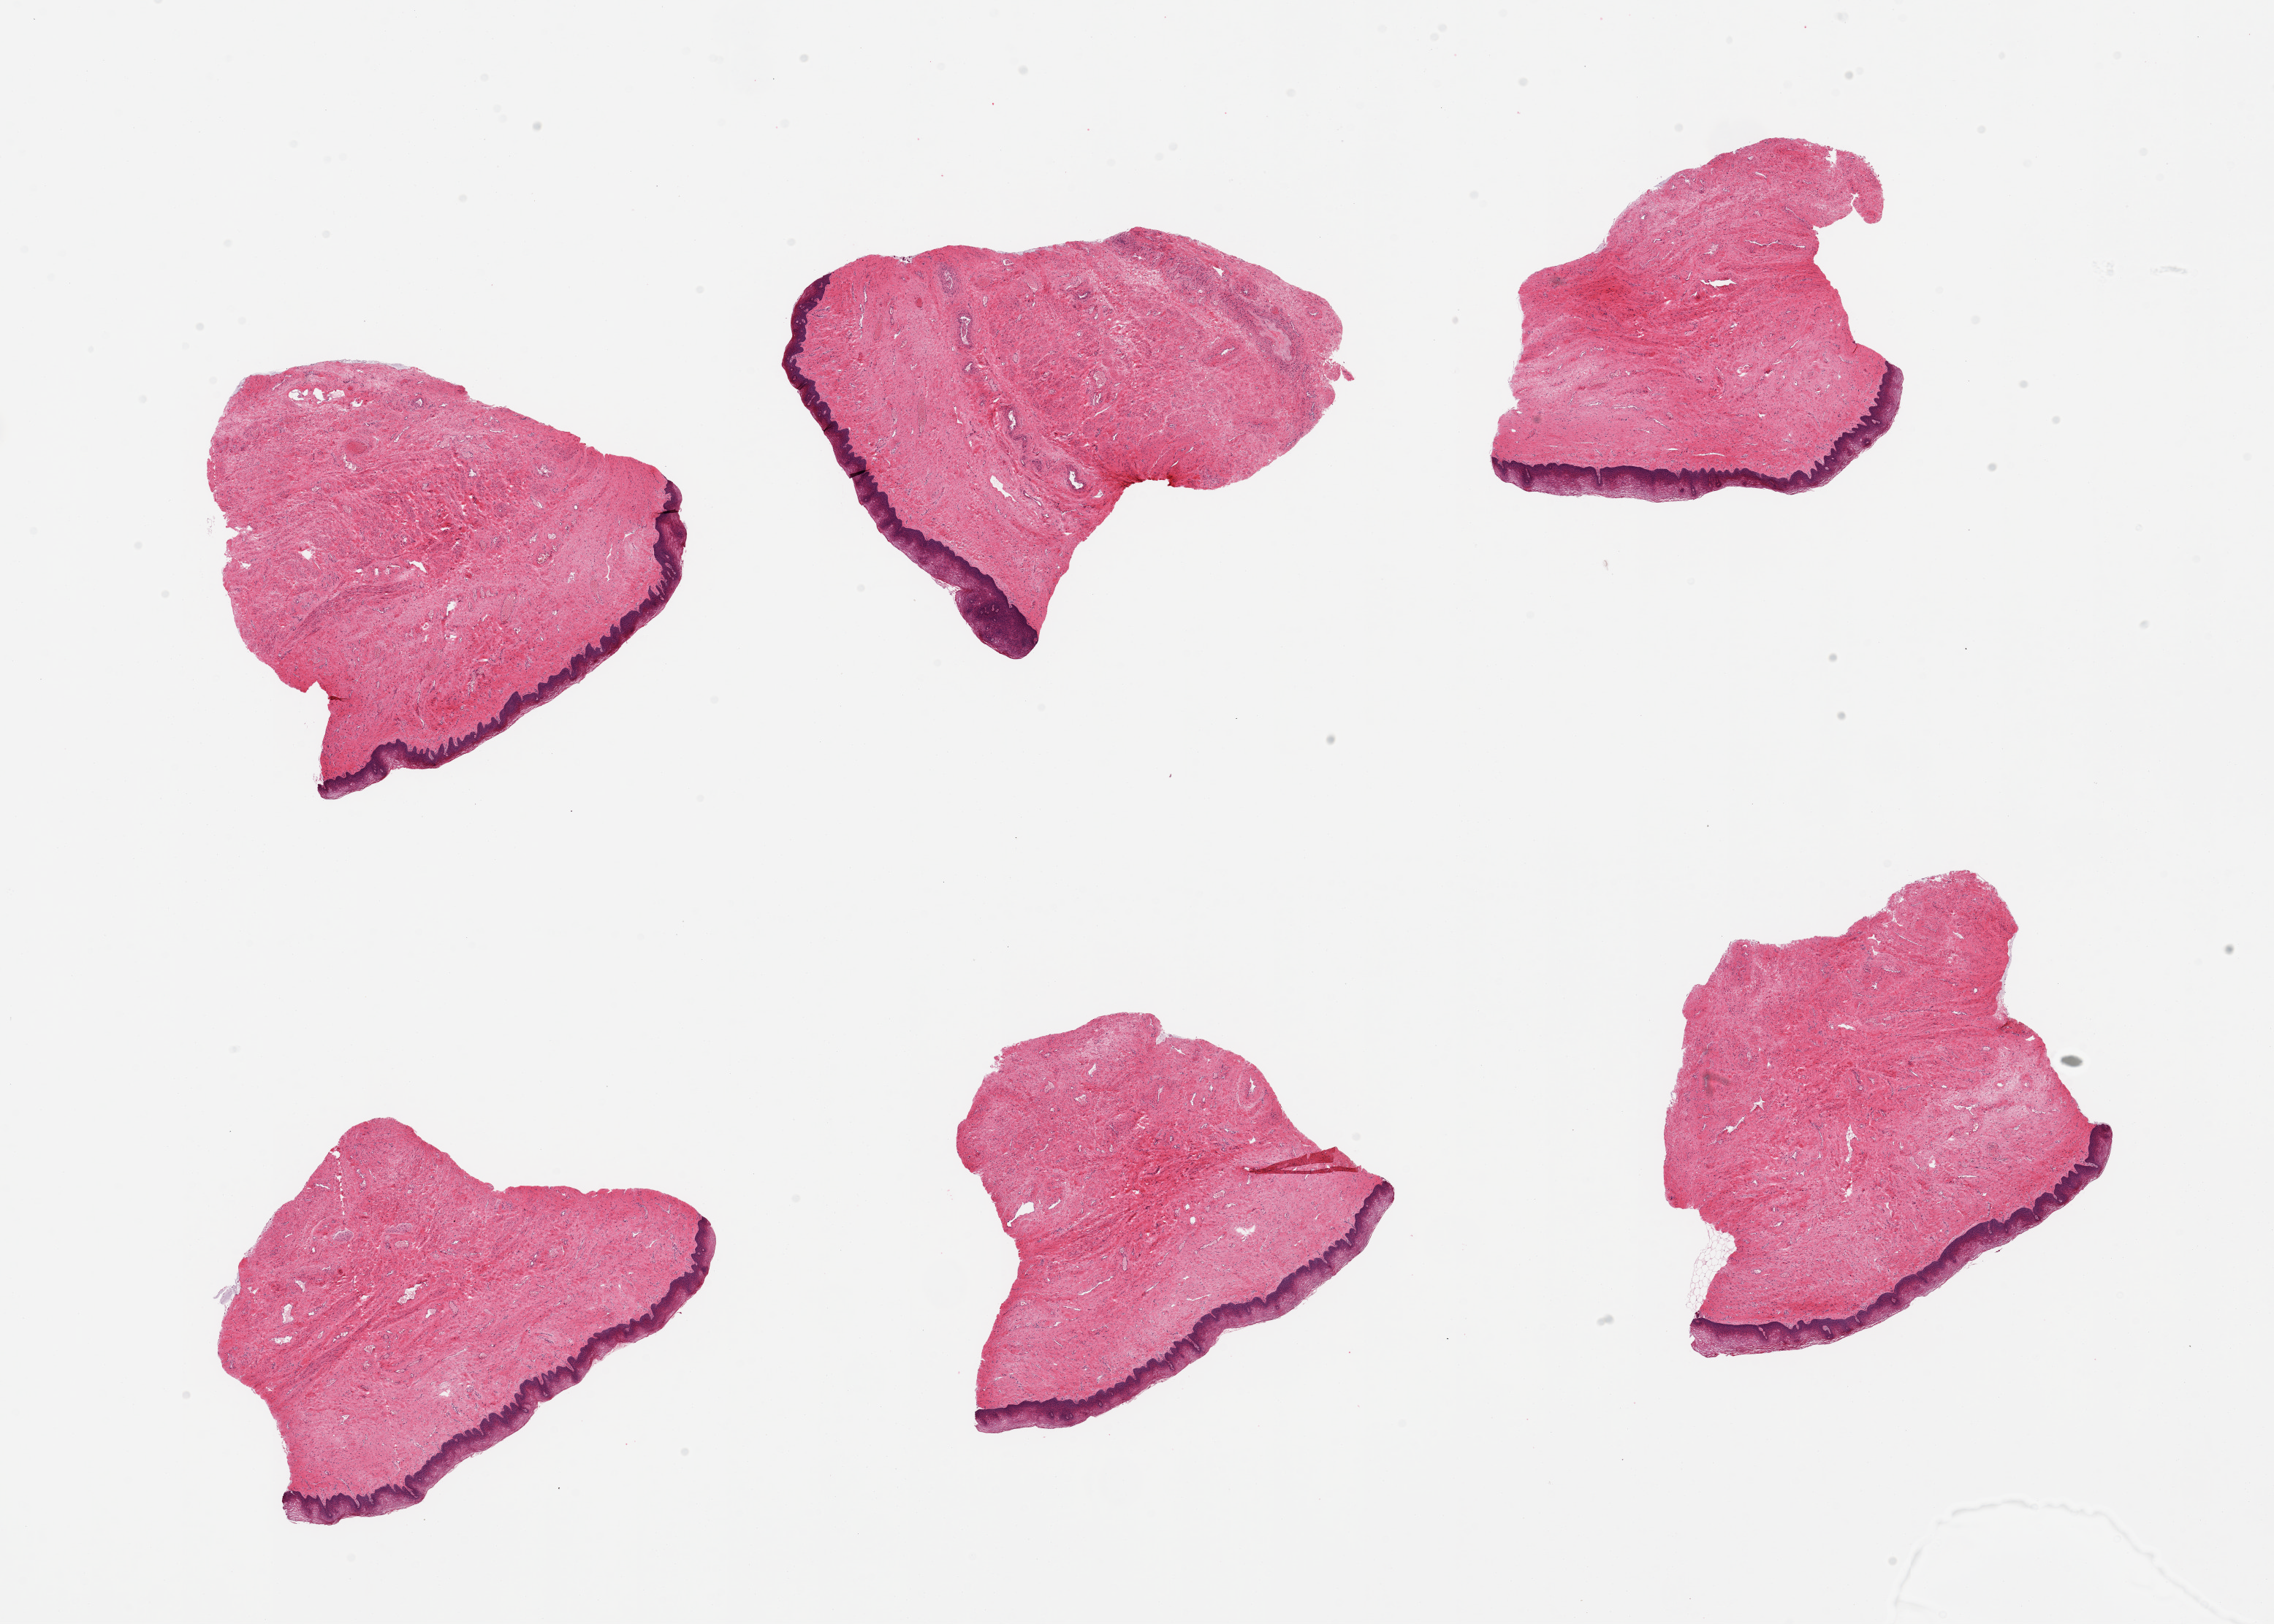
Digitized haematoxylin and eosin-stained section, brightfield, shown as a low-resolution overview of the whole scanned area (about 24.6 x 17.6 mm, acquisition: 20x scan), PAXgene-fixed paraffin-embedded (PFPE) section, target tissue: vagina, tissue donor sample. Donor sex: female.
Review note (as recorded): 6 pieces.